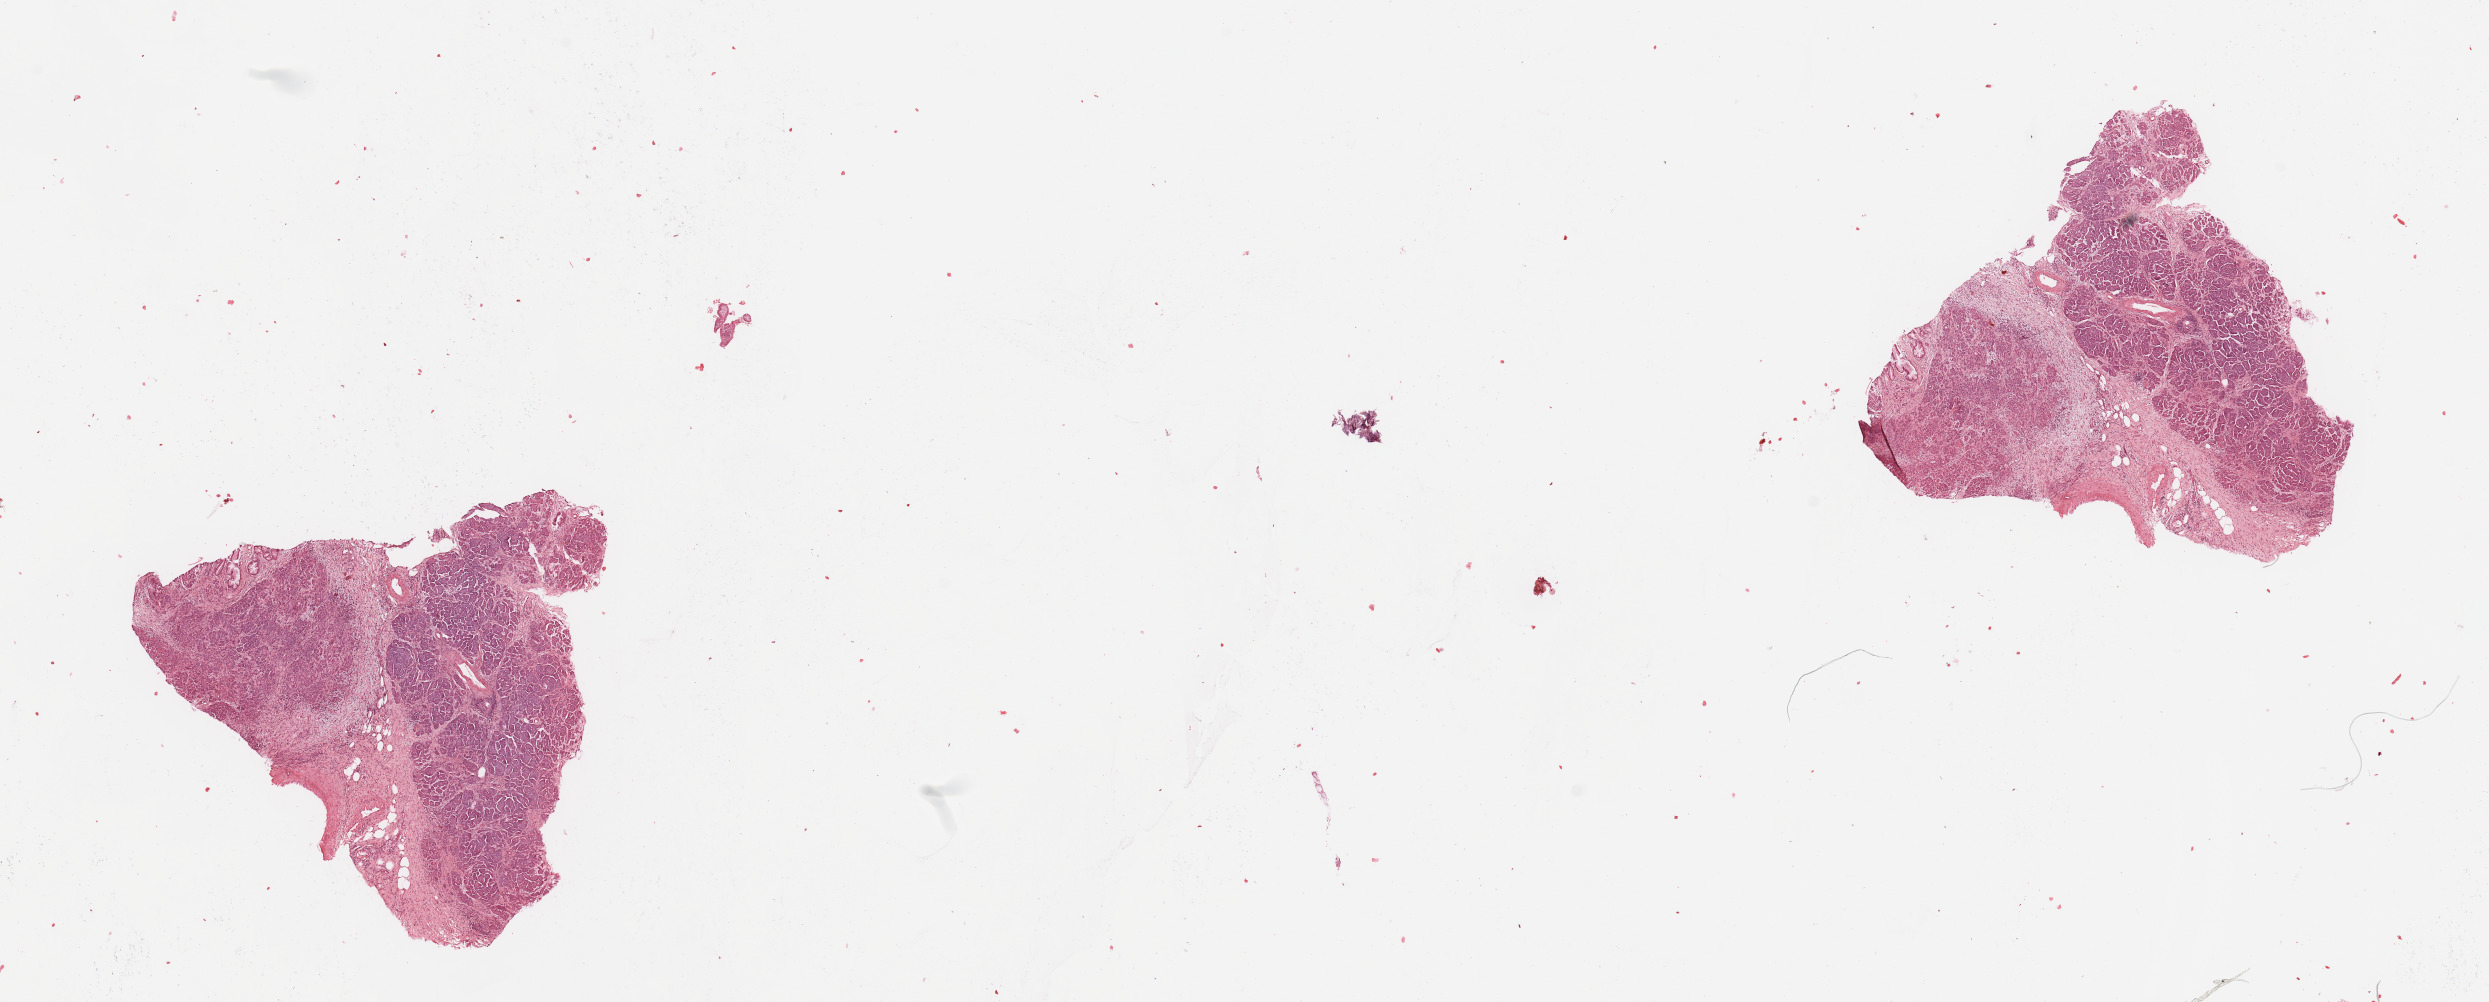
H&E whole-slide image — shown as a low-resolution overview of the whole scanned area (about 19.7 x 7.9 mm). Normal (non-tumour) tissue sample, sampled site: pancreas. Patient: female, age 69 years.
This section: normal (non-tumour) tissue from the same patient. Patient diagnosis: Infiltrating duct carcinoma, NOS.